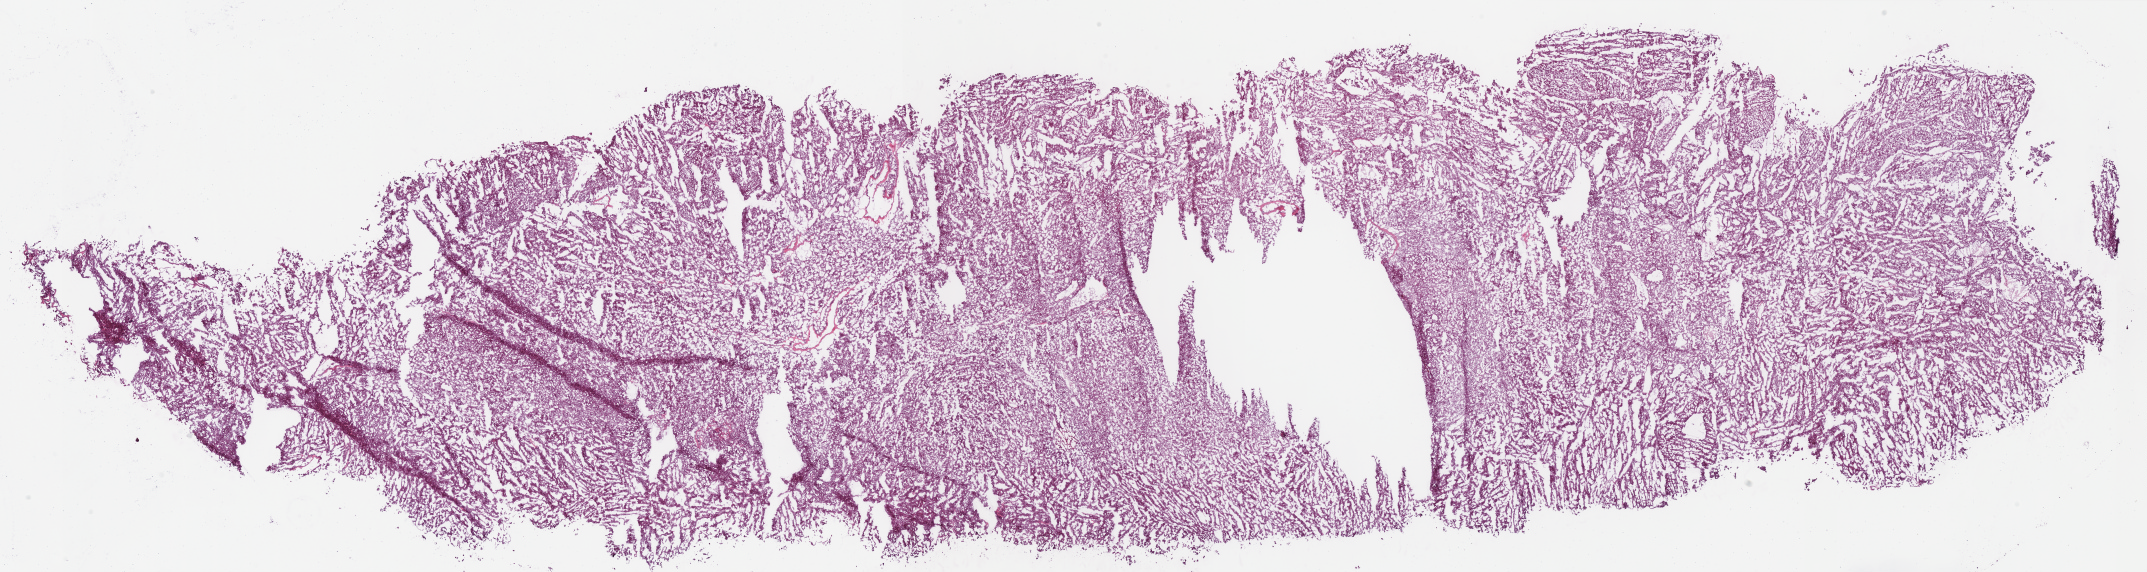
H&E-stained whole-slide image — low-resolution overview of the scanned area, about 33.8 x 9.0 mm, frozen section from the bottom of the tissue portion, primary tumour sample from the kidney. Patient: male, age at initial diagnosis 69 years. Composition of this section per pathologist review: tumour cells 90%, tumour nuclei 90%, normal cells 0%, stromal cells 10%, necrosis 0%.
Histologic diagnosis: Renal cell carcinoma, chromophobe type. AJCC pathologic stage: II (7th edition). Lymph nodes positive (case pathology): 0 of 1 examined. Laterality: left.